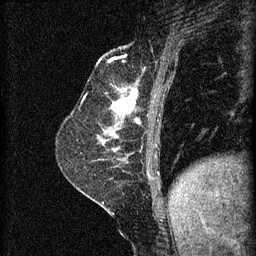
Breast MRI (dynamic contrast-enhanced), one sagittal slice; slice 22 of 60 in the series (ordered by position); 3 images stored at this slice position (order not interpretable as contrast timing); 1.5 T; TE 4.2 ms, TR 8.2 ms; 256 × 256 image matrix, field of view 180 × 180 mm. Patient: female, 59 years.
Outlined on this slice (semi-automatic segmentation, software-assisted and operator-edited):
- analysis volume of interest (the breast-tissue region the enhancement analysis was run in; not a lesion): bounding box [x1, y1, x2, y2] px = [98, 92, 137, 135]
- tumour enhancement mask (voxels above the 70 % enhancement threshold inside the analysis volume of interest): [112, 92, 137, 117]